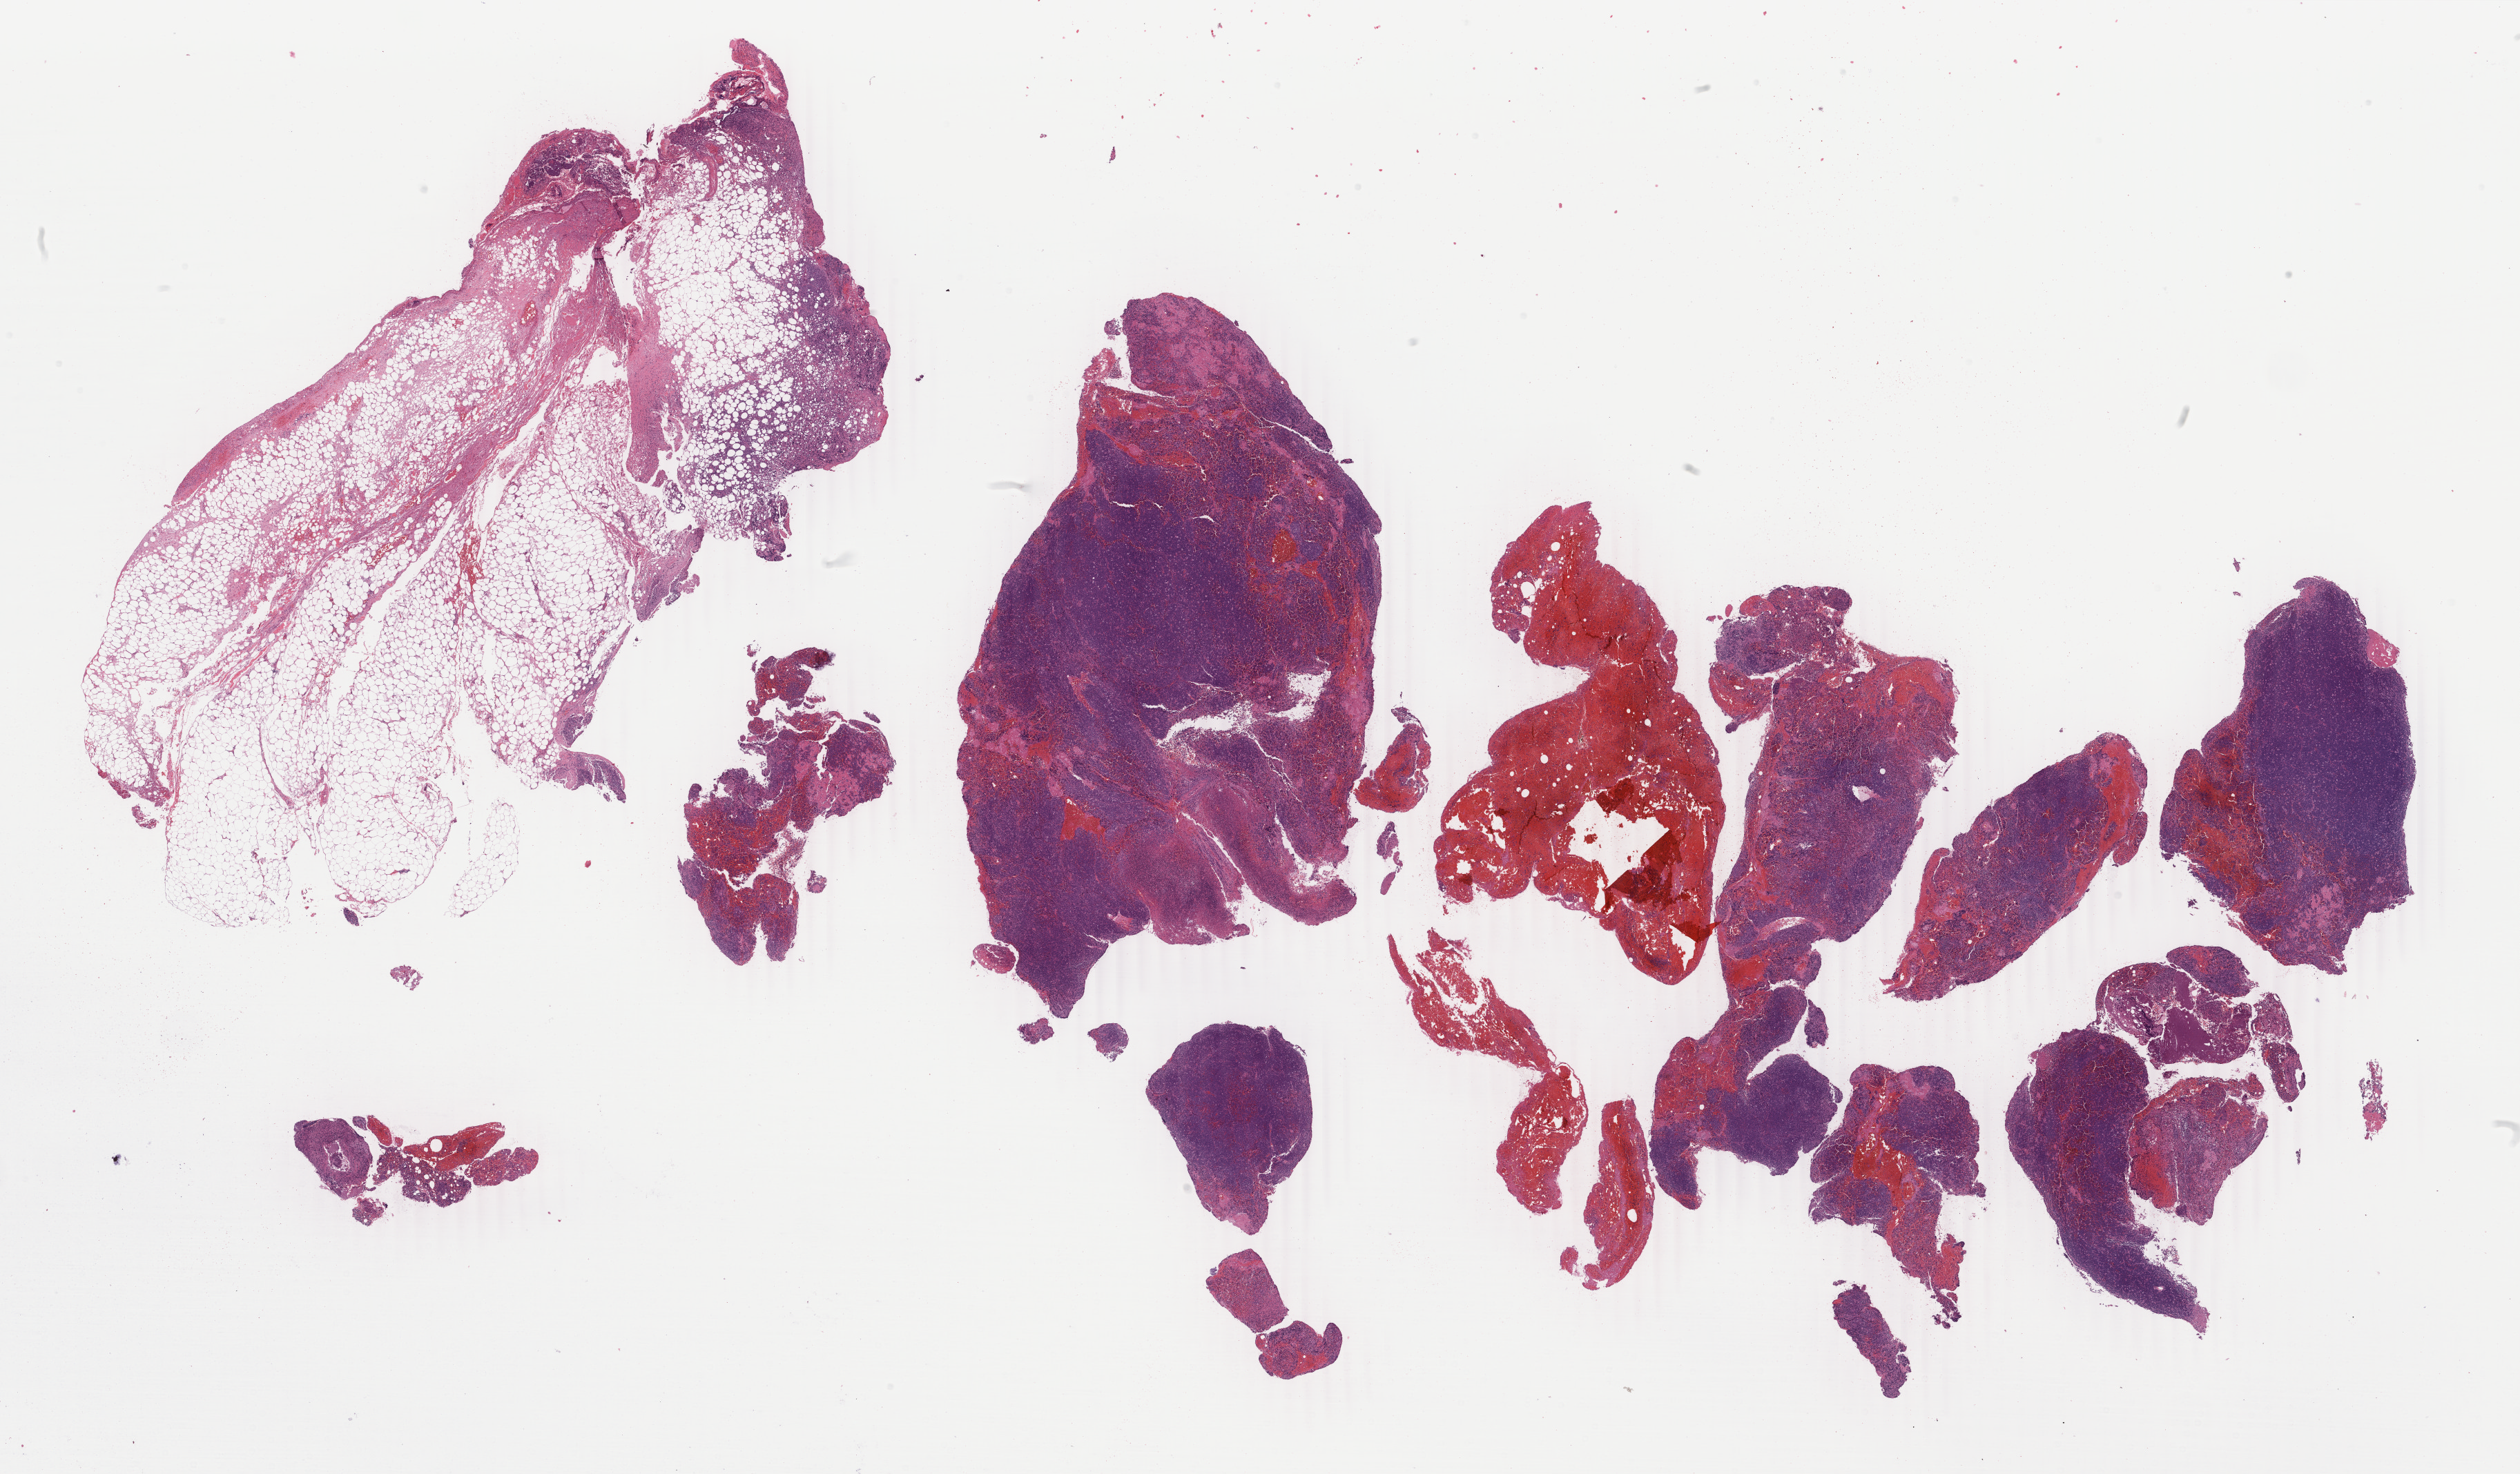
Digitized haematoxylin and eosin-stained section, low-resolution overview of the scanned area, about 29.0 x 17.0 mm; tumor tissue; site: abdominal lymph node. Patient male; aged 27.
Diagnosis: Burkitt lymphoma, NOS.